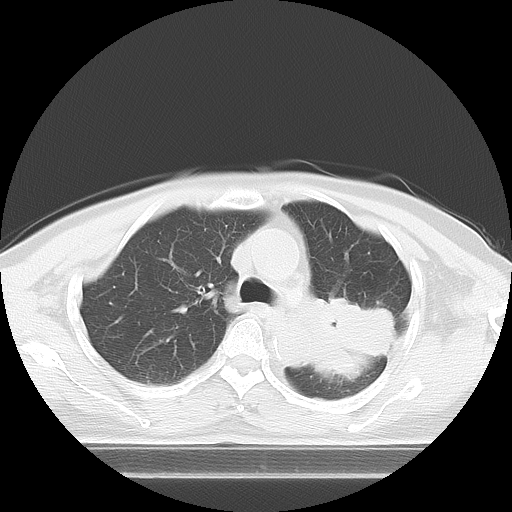
Chest CT, one axial slice; position 5 of 21 along the scan axis; reconstruction kernel LUNG; 120 kVp; lung window (W 1500 / L -600 HU); 5 mm slice thickness; 512 × 512 image matrix, field of view 350 × 350 mm. Patient: female, 74 years. From the clinical record (not read from this slice): clinical TNM (as recorded): T3 N1 M1c; histopathological grade: G3.
Structures marked on this image (rectangle marked by the reading radiologist):
- lung tumour (recorded histology: small cell carcinoma): bounding box (x1, y1, x2, y2) in pixels: (304, 287, 409, 389)